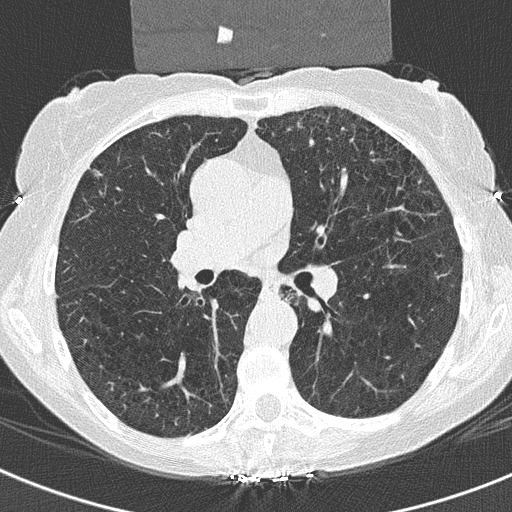
Low-dose screening chest CT, axial slice; third annual screen; lung window (W 1500 / L -600 HU); 2 mm slice thickness; lung (sharp) reconstruction kernel (B50f); 120 kVp; slice 129 of 325 in the series. Female, age 70 years at enrolment. Current smoker at enrolment.
• Expert-annotated lung lesion, bounding box <83,159,110,190> (left, top, right, bottom; pixels).
• Screening reader's record for this exam (one nodule recorded; not confirmed to be the boxed lesion): non-calcified nodule or mass ≥4 mm, right middle lobe, 5 × 5 mm, spiculated (stellate) margins, ground glass attenuation, pre-existing on the prior screen: no.
• Official screen result: positive, other.
• Participant outcome: lung cancer diagnosed 321 days after this screen — adenosquamous carcinoma, right upper lobe, poorly differentiated (G3), stage IA (AJCC 6th edition), 12 mm at pathology.